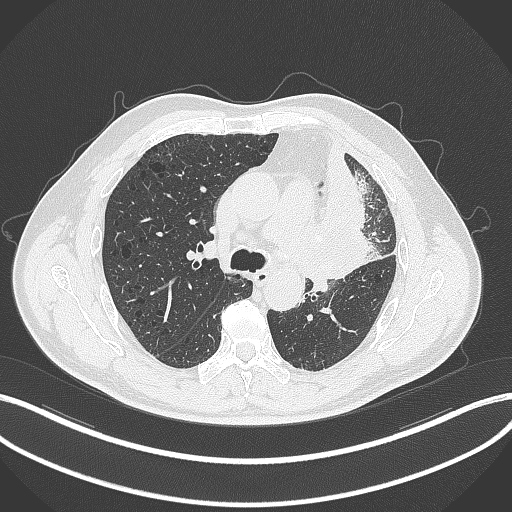
Chest CT, one axial slice. Position 196 of 297 along the scan axis. Lung window (W 1500 / L -600 HU). 1 mm slice thickness. 512 × 512 image matrix, field of view 400 × 400 mm. Patient: male, 68 years. Case-level facts recorded for this patient, not image findings: clinical TNM (as recorded): T3 N3 M1.
Structures marked on this image (rectangle marked by the reading radiologist):
- lung tumour (recorded histology: adenocarcinoma): bounding box <309,159,379,290> (left, top, right, bottom; pixels)